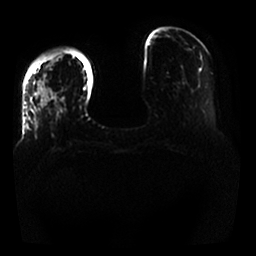
Breast MRI, one axial slice. Slice 4 of 25 in the series (ordered by position). Diffusion-weighted series; image 2 of 4 stored at this slice position (different b-values; order by instance number). 1.5 T. 4 mm slice thickness. 256 × 256 image matrix, field of view 350 × 350 mm. Female patient.
Outlined on this slice (outlined manually by an expert reader):
- tumour on diffusion-weighted imaging: bounding box <38,84,51,106> (left, top, right, bottom; pixels)